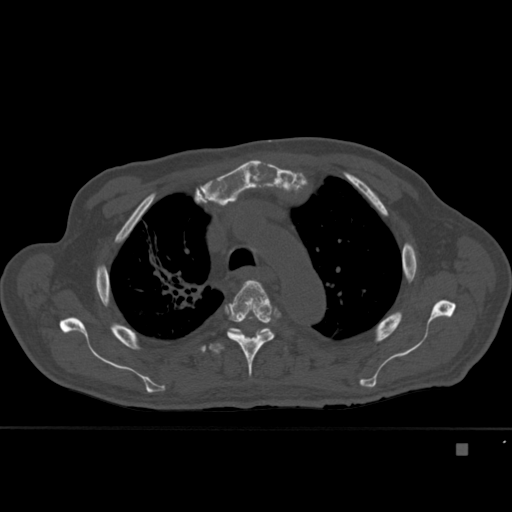
CT including the spine, one axial slice. Slice 319 of 451 in the series (ordered by position). Bone window (W 1800 / L 400 HU). 1.5 mm slice thickness. 512 × 512 image matrix. Male patient, age 75 years. Case-level facts recorded for this patient, not image findings: primary cancer: prostate.
Outlined on this slice (semi-automatic segmentation, software-assisted and operator-edited):
- T3 vertebra: box from (x=255, y=330) to (x=259, y=335) px
- T4 vertebra: (x=227, y=280)–(x=275, y=377)
- T5 vertebra: (x=209, y=328)–(x=287, y=354)